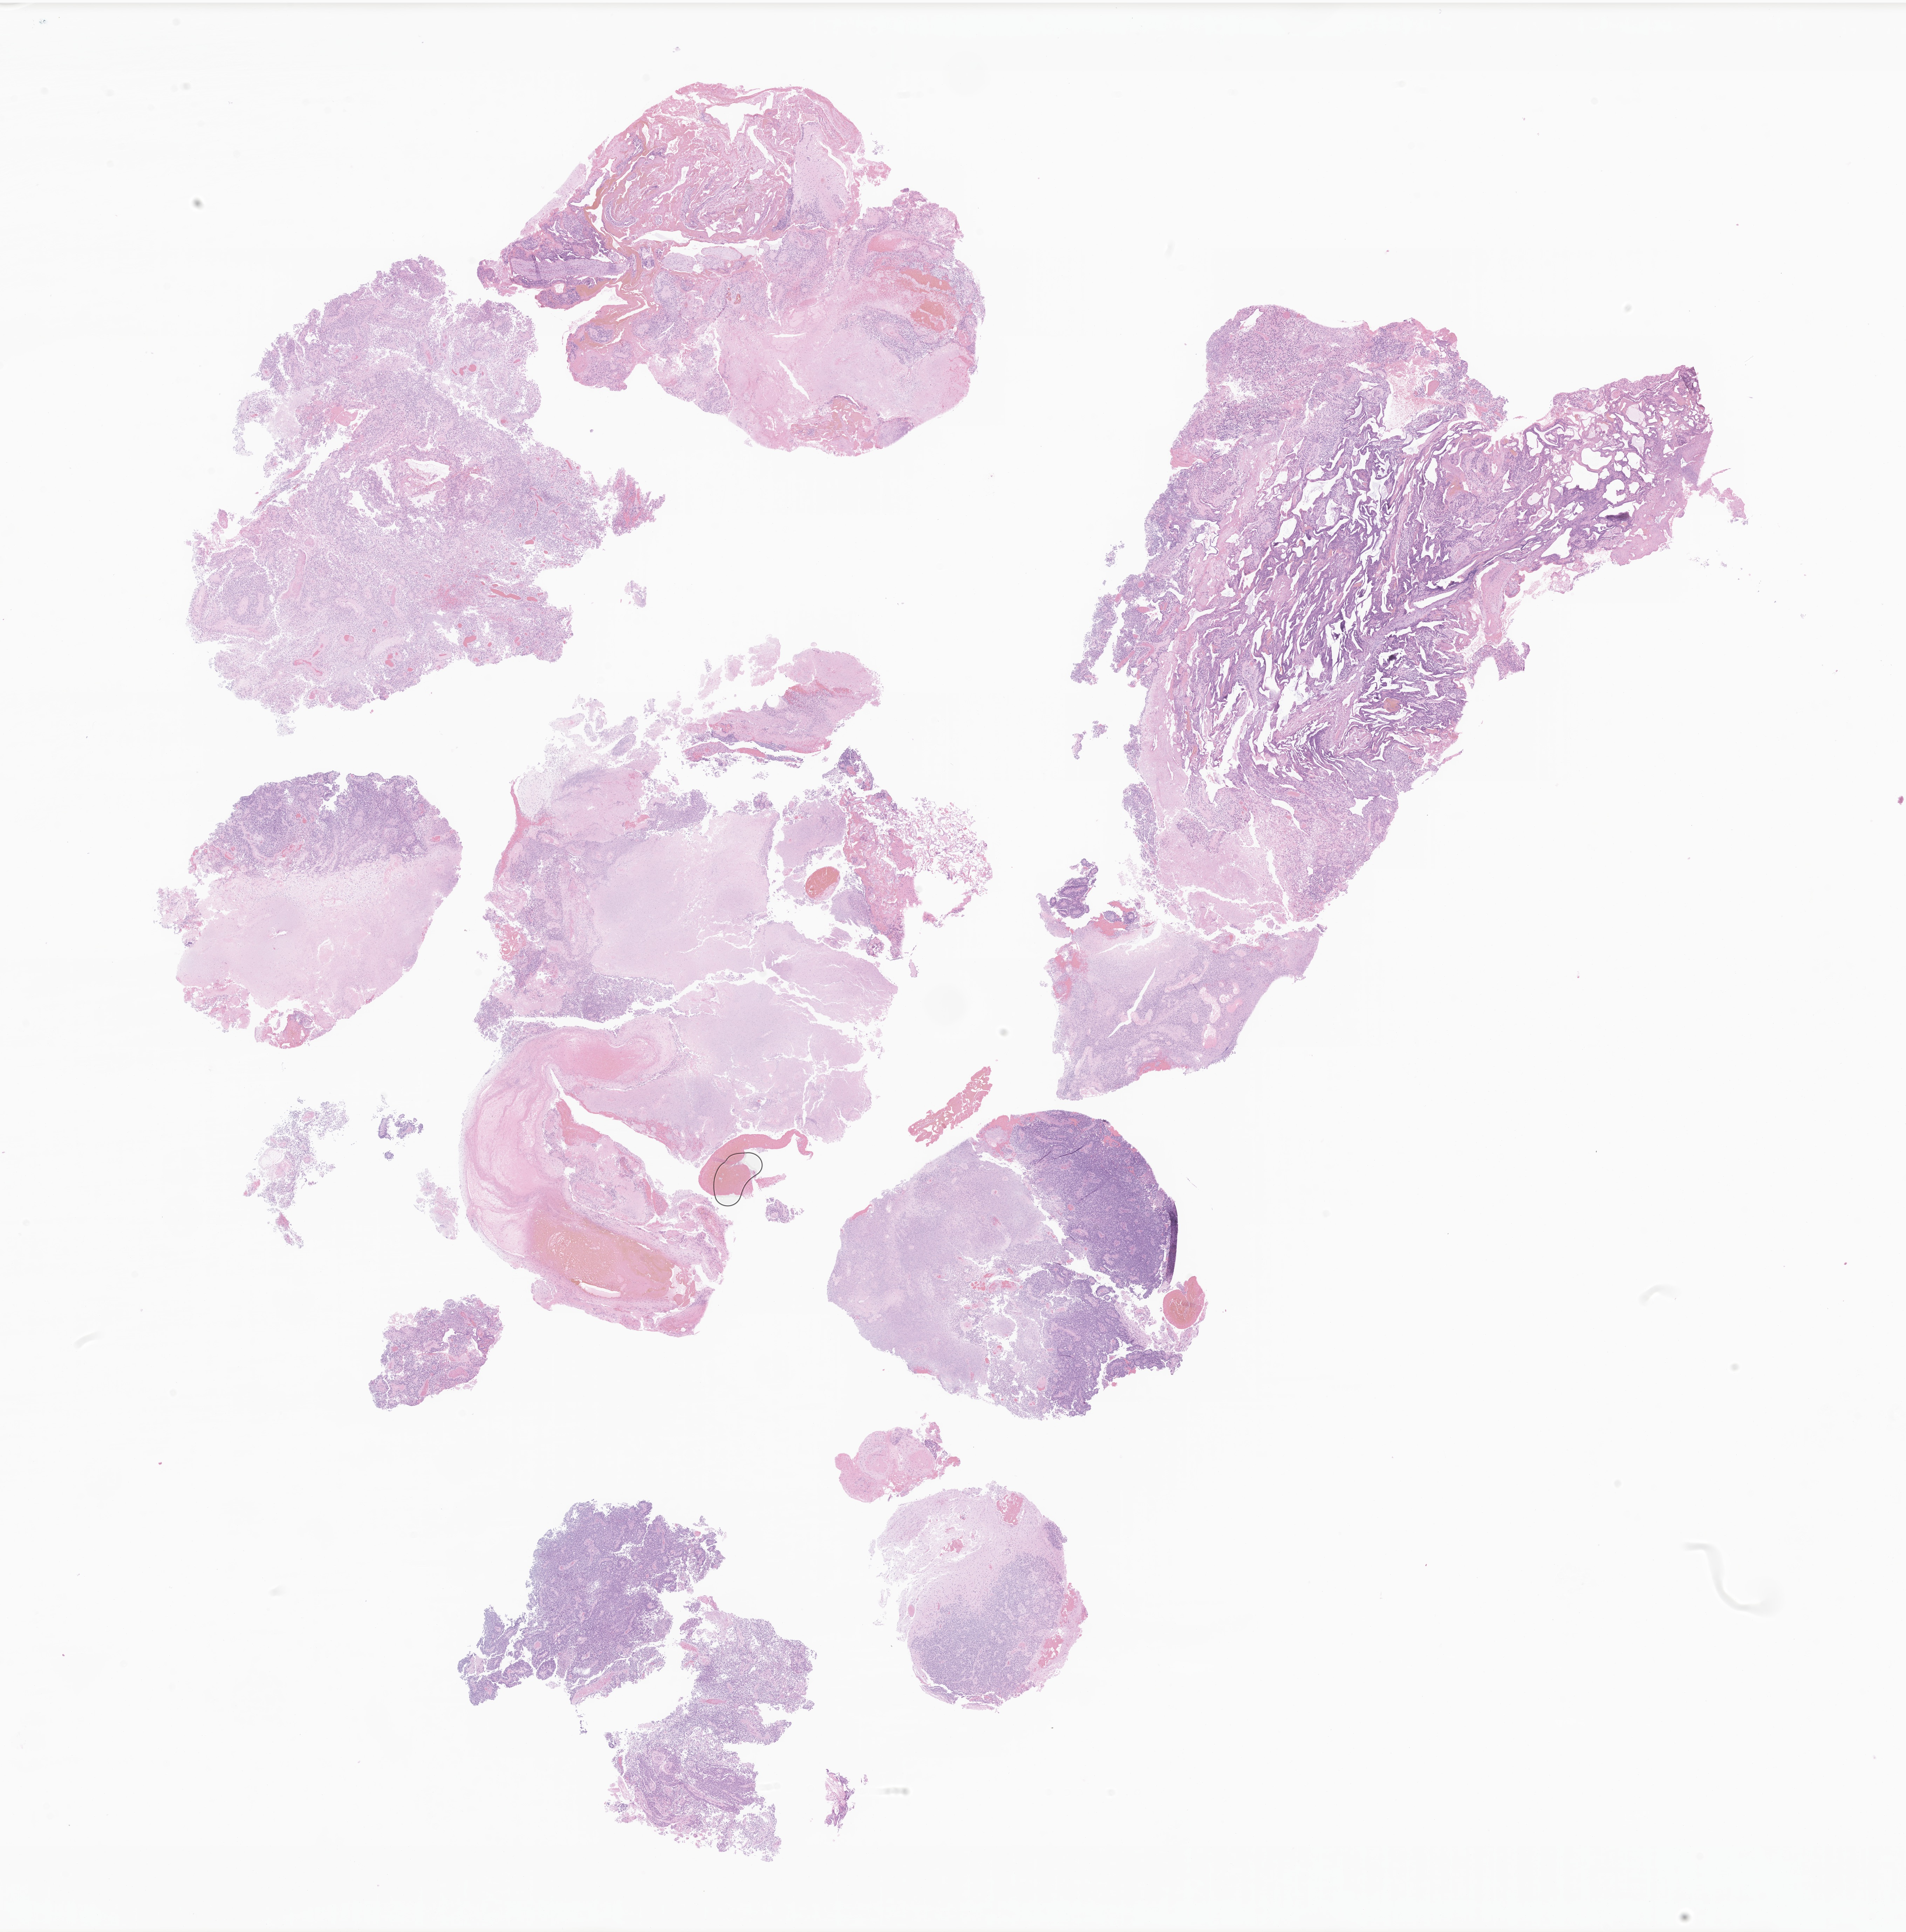
Whole-slide image, hematoxylin and eosin (H&E) stain of tumor tissue from the brain, whole scanned area (about 22.9 x 23.2 mm) shown as a low-resolution overview. FFPE section. Female patient, age 65 months (5 years 5 months).
Recorded diagnosis: Neoplasm, malignant.